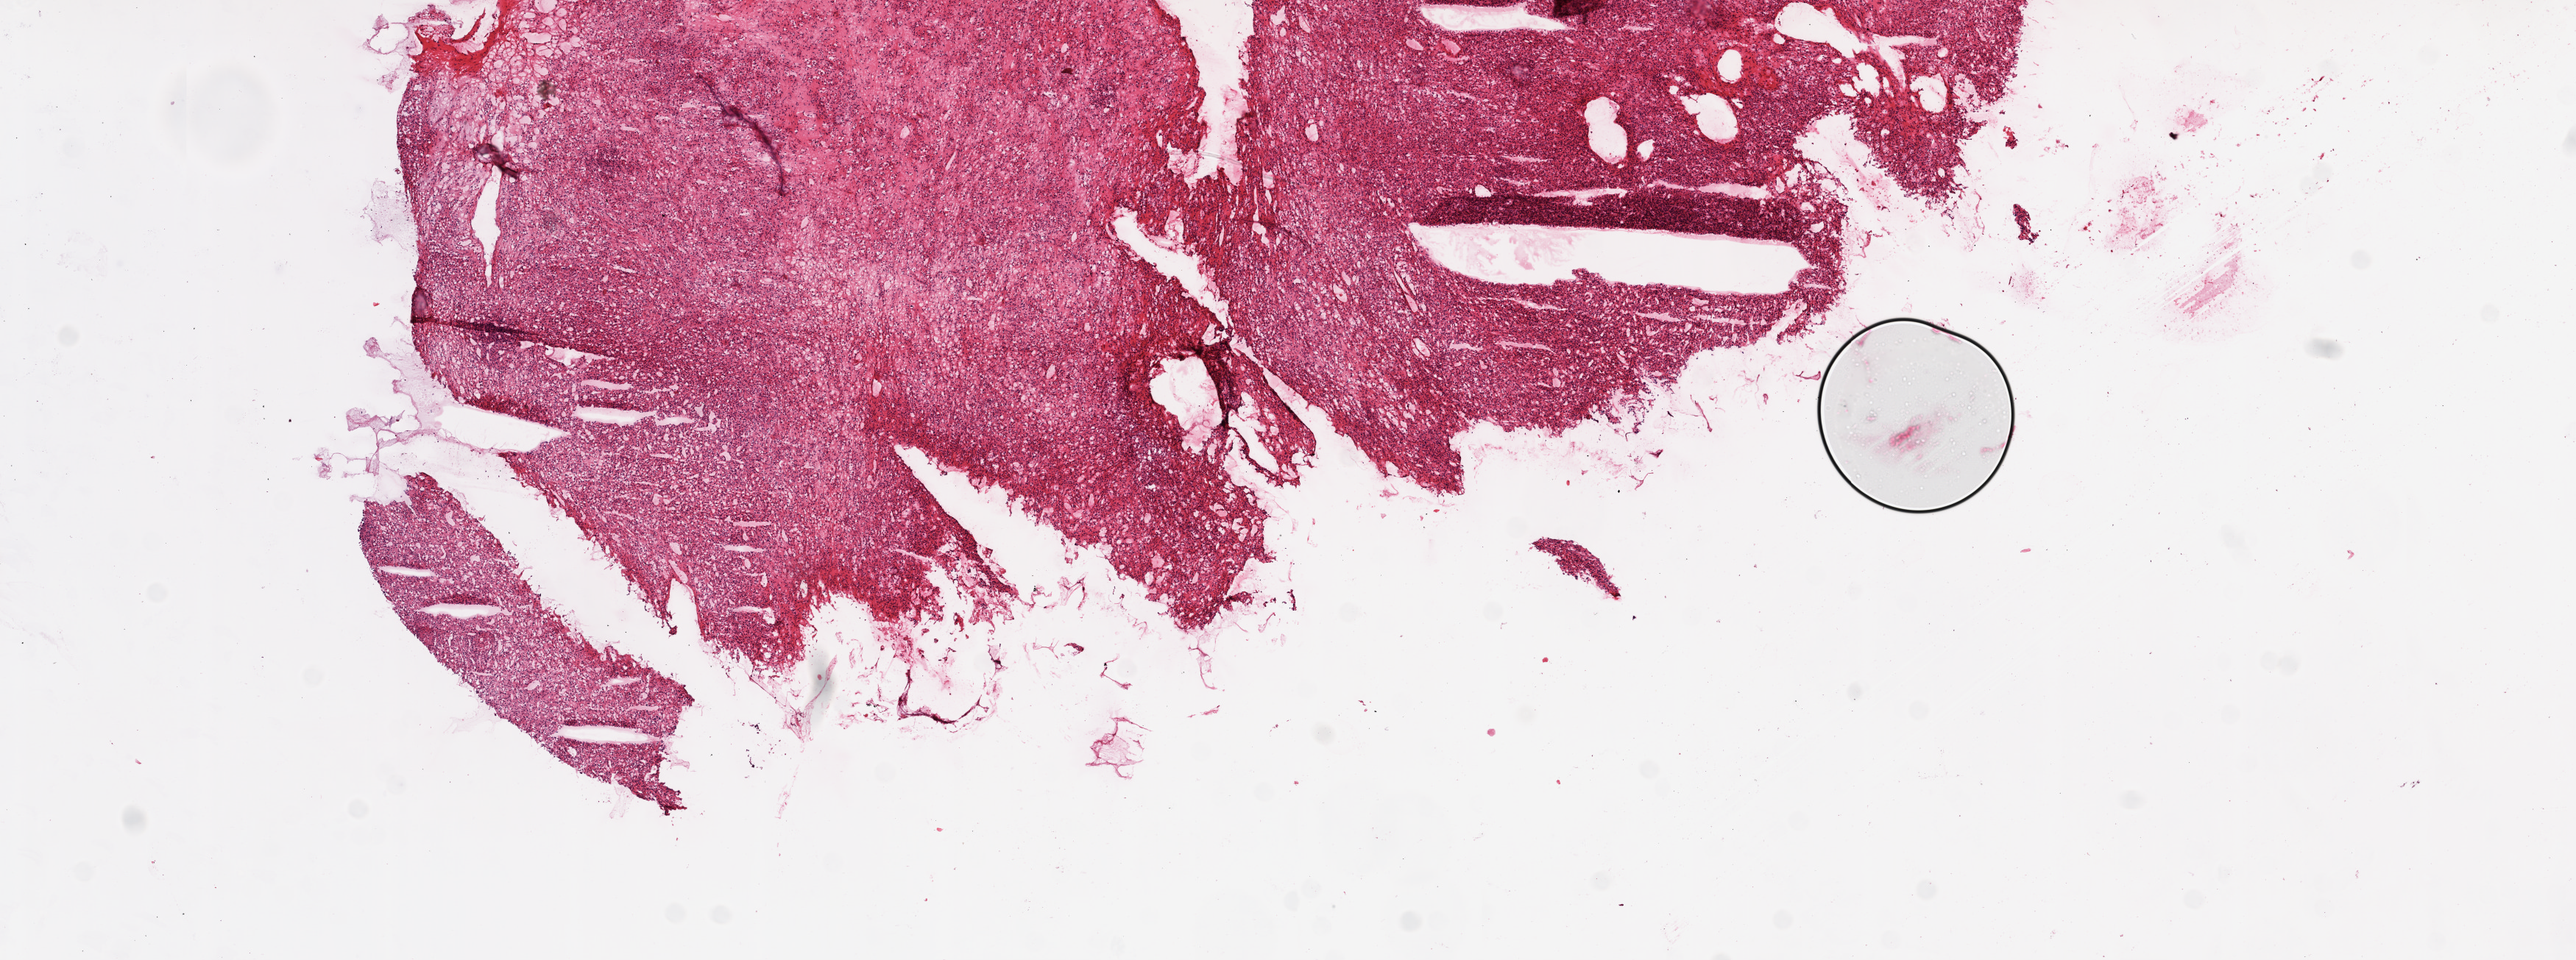
Digitized H&E tissue section (whole slide), whole scanned area (about 14.0 x 5.2 mm) shown as a low-resolution overview; frozen section; primary tumour sample from the kidney. Patient: male, age at initial diagnosis 43 years. Histologic grade: G3 (poorly differentiated). Pathologist review of this section (percent, as recorded): tumour cells 90%, tumour nuclei 85%, normal cells 0%, stromal cells 10%, necrosis 0%.
* histologic diagnosis: Clear cell adenocarcinoma, NOS
* laterality: left
* AJCC pathologic stage: IV (6th edition)